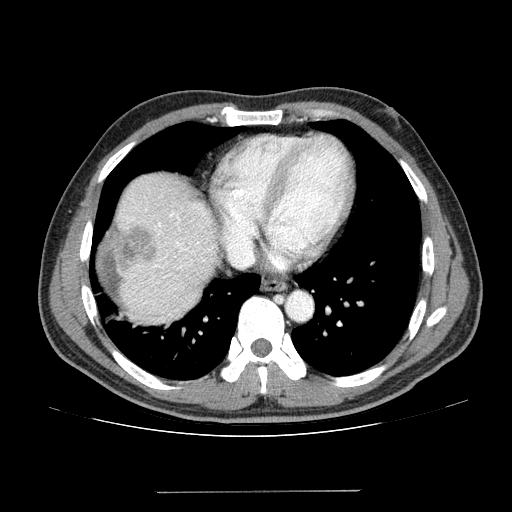
Contrast-enhanced abdominal CT (liver protocol), one axial slice; position 120 of 131 along the scan axis; reconstruction kernel STANDARD; one of 2 acquisitions stored at this slice position; soft-tissue window (W 400 / L 40 HU); 2.5 mm slice thickness; 512 × 512 image matrix, field of view 380 × 380 mm. From the clinical record (not read from this slice): diagnosis: hepatocellular carcinoma (patient treated with transarterial chemoembolisation; whether this scan precedes or follows treatment is not stated here); TNM stage (as recorded): Stage-I; Child-Pugh class: A; tumour differentiation: poorly differentiated.
Structures marked on this image (semi-automatically segmented with operator editing):
- liver parenchyma outside the tumour (the mass and vessels are separate outlines, so this box may not span the whole liver): bounding box (x1, y1, x2, y2) in pixels: (98, 172, 216, 322)
- mass: (97, 222, 155, 273)
- liver vessels: (126, 212, 205, 304)